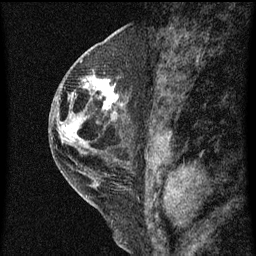
Breast MRI (dynamic contrast-enhanced), one sagittal slice. Position 27 of 60 along the scan axis. Dynamic contrast-enhanced series, image 2 of 3 at this slice position (ordered by acquisition). 1.5 T. TE 4.2 ms, TR 8 ms. 2 mm slice thickness. 256 × 256 image matrix, field of view 180 × 180 mm. Patient: female, 48 years.
Structures marked on this image (semi-automatically segmented with operator editing):
- analysis volume of interest (the breast-tissue region the enhancement analysis was run in; not a lesion): box from (x=89, y=72) to (x=123, y=113) px
- tumour enhancement mask (voxels above the 70 % enhancement threshold inside the analysis volume of interest): (x=89, y=78)–(x=120, y=113)